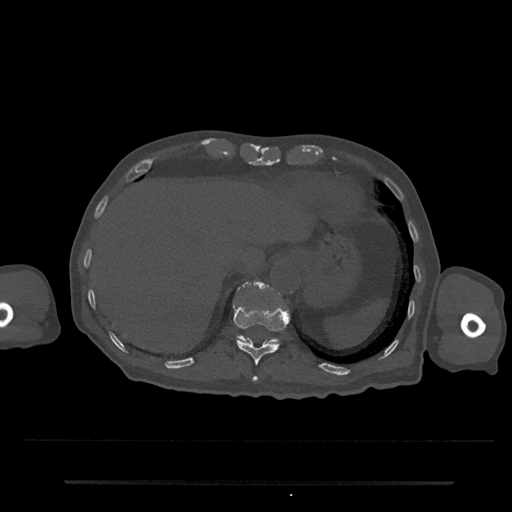
CT including the spine, one axial slice; slice 244 of 797 in the series (ordered by position); bone window (W 1800 / L 400 HU); 0.5 mm slice thickness; 512 × 512 image matrix, field of view 427 × 427 mm. Male patient, age 74 years. Case-level facts recorded for this patient, not image findings: primary cancer: prostate.
Annotated regions visible in this slice (semi-automatic segmentation, software-assisted and operator-edited):
- T11 vertebra: bounding box (x1, y1, x2, y2) in pixels: (233, 304, 289, 380)
- T12 vertebra: (237, 284, 279, 344)